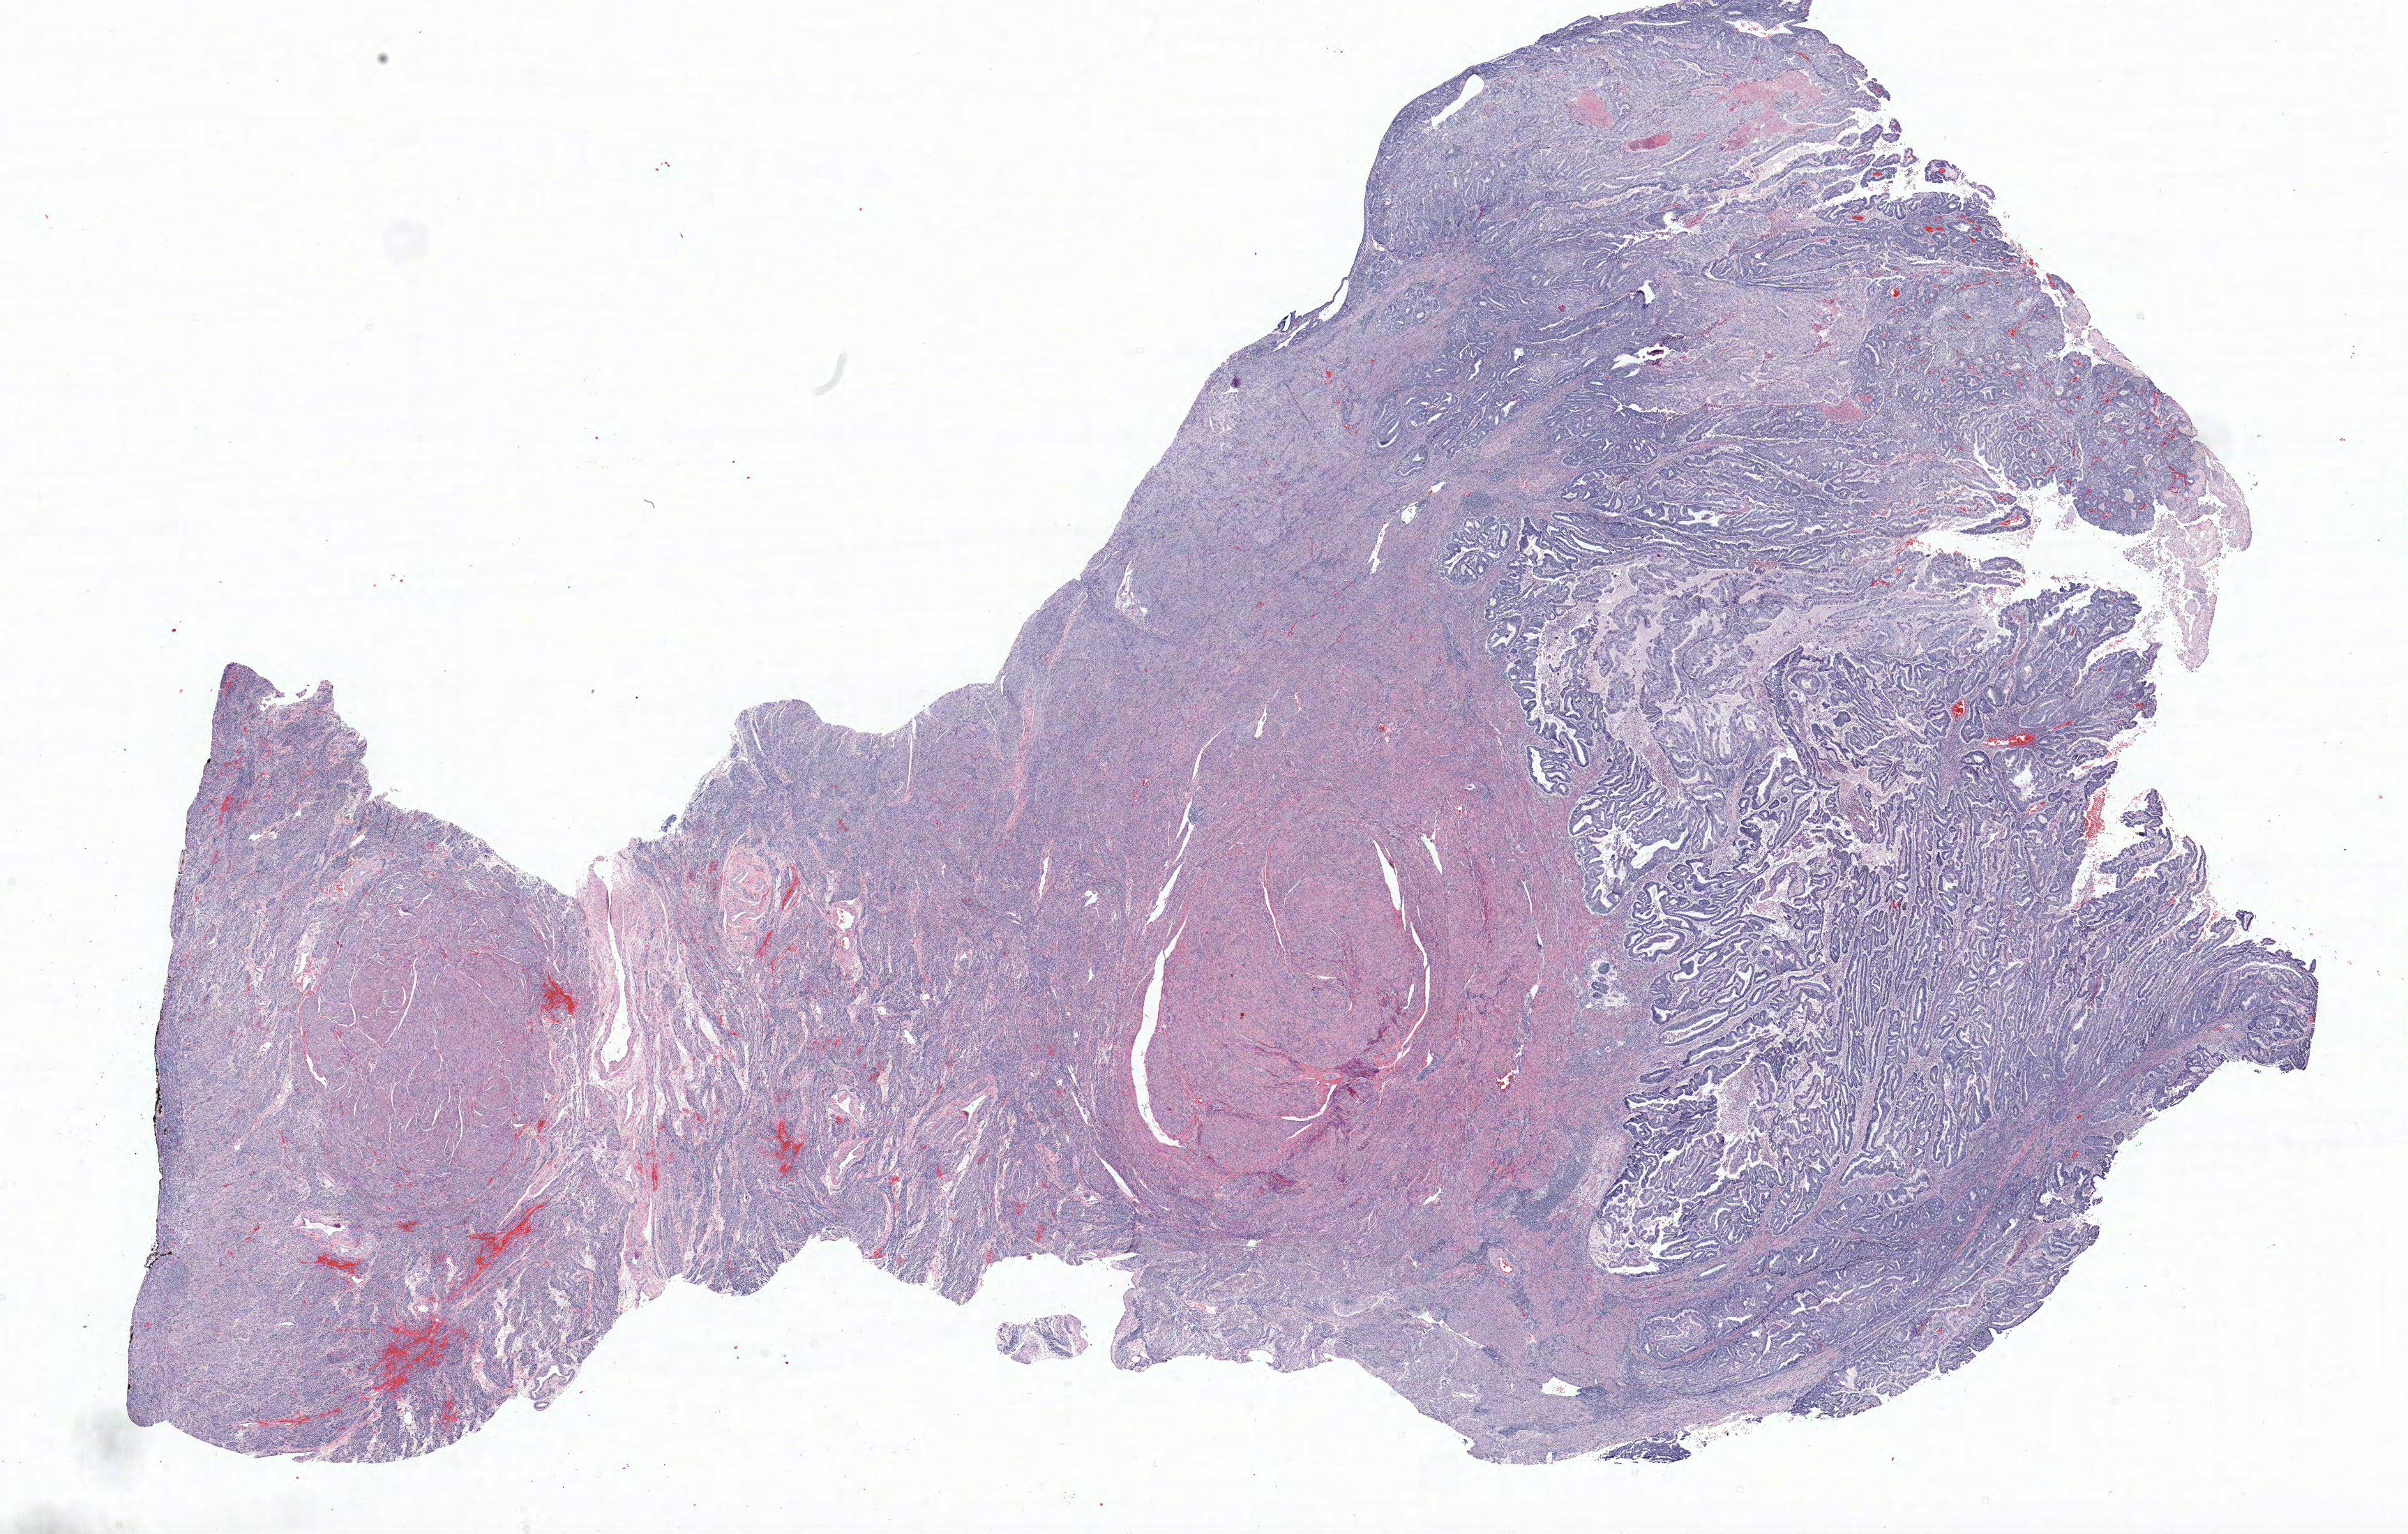
Whole-slide histology image, H&E-stained, whole scanned area (about 27.8 x 17.7 mm, acquisition: 20x scan) shown as a low-resolution overview, formalin-fixed paraffin-embedded (FFPE) diagnostic section, uterus, primary tumour sample. Patient: female, age at initial diagnosis 63 years. Histologic grade: G2 (moderately differentiated).
Diagnosis: Endometrioid adenocarcinoma, NOS (endometrium). FIGO stage: IA. Lymph nodes positive (case pathology): 0 of 14 examined.